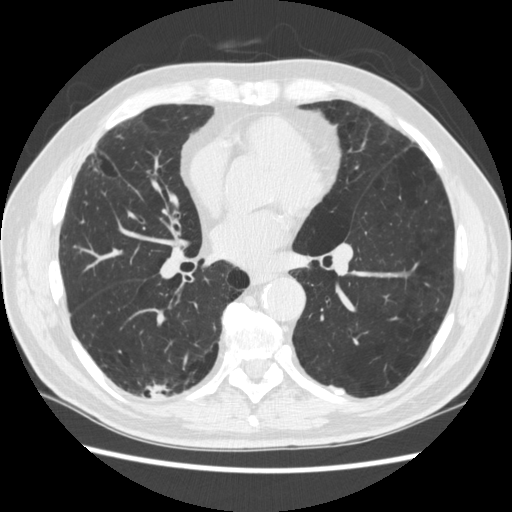
Low-dose screening chest CT, axial slice; third screening round (two years after baseline); lung window (W 1500 / L -600 HU); 1.25 mm slice thickness; standard (soft-tissue) reconstruction kernel (STANDARD); 120 kVp; slice 140 of 266 in the series. Male participant, aged 70 years at enrolment.
Expert-annotated lung lesion, box from (x=120, y=361) to (x=186, y=421) px. The screening reader recorded 4 non-calcified nodules or masses ≥4 mm on this exam (right lower lobe, right lower lobe, left lower lobe, left lower lobe); which of them this box marks is not recorded. Participant outcome: lung cancer diagnosed 253 days after this screen — squamous cell carcinoma, NOS, right upper lobe, poorly differentiated (G3), stage IV (AJCC 6th edition).